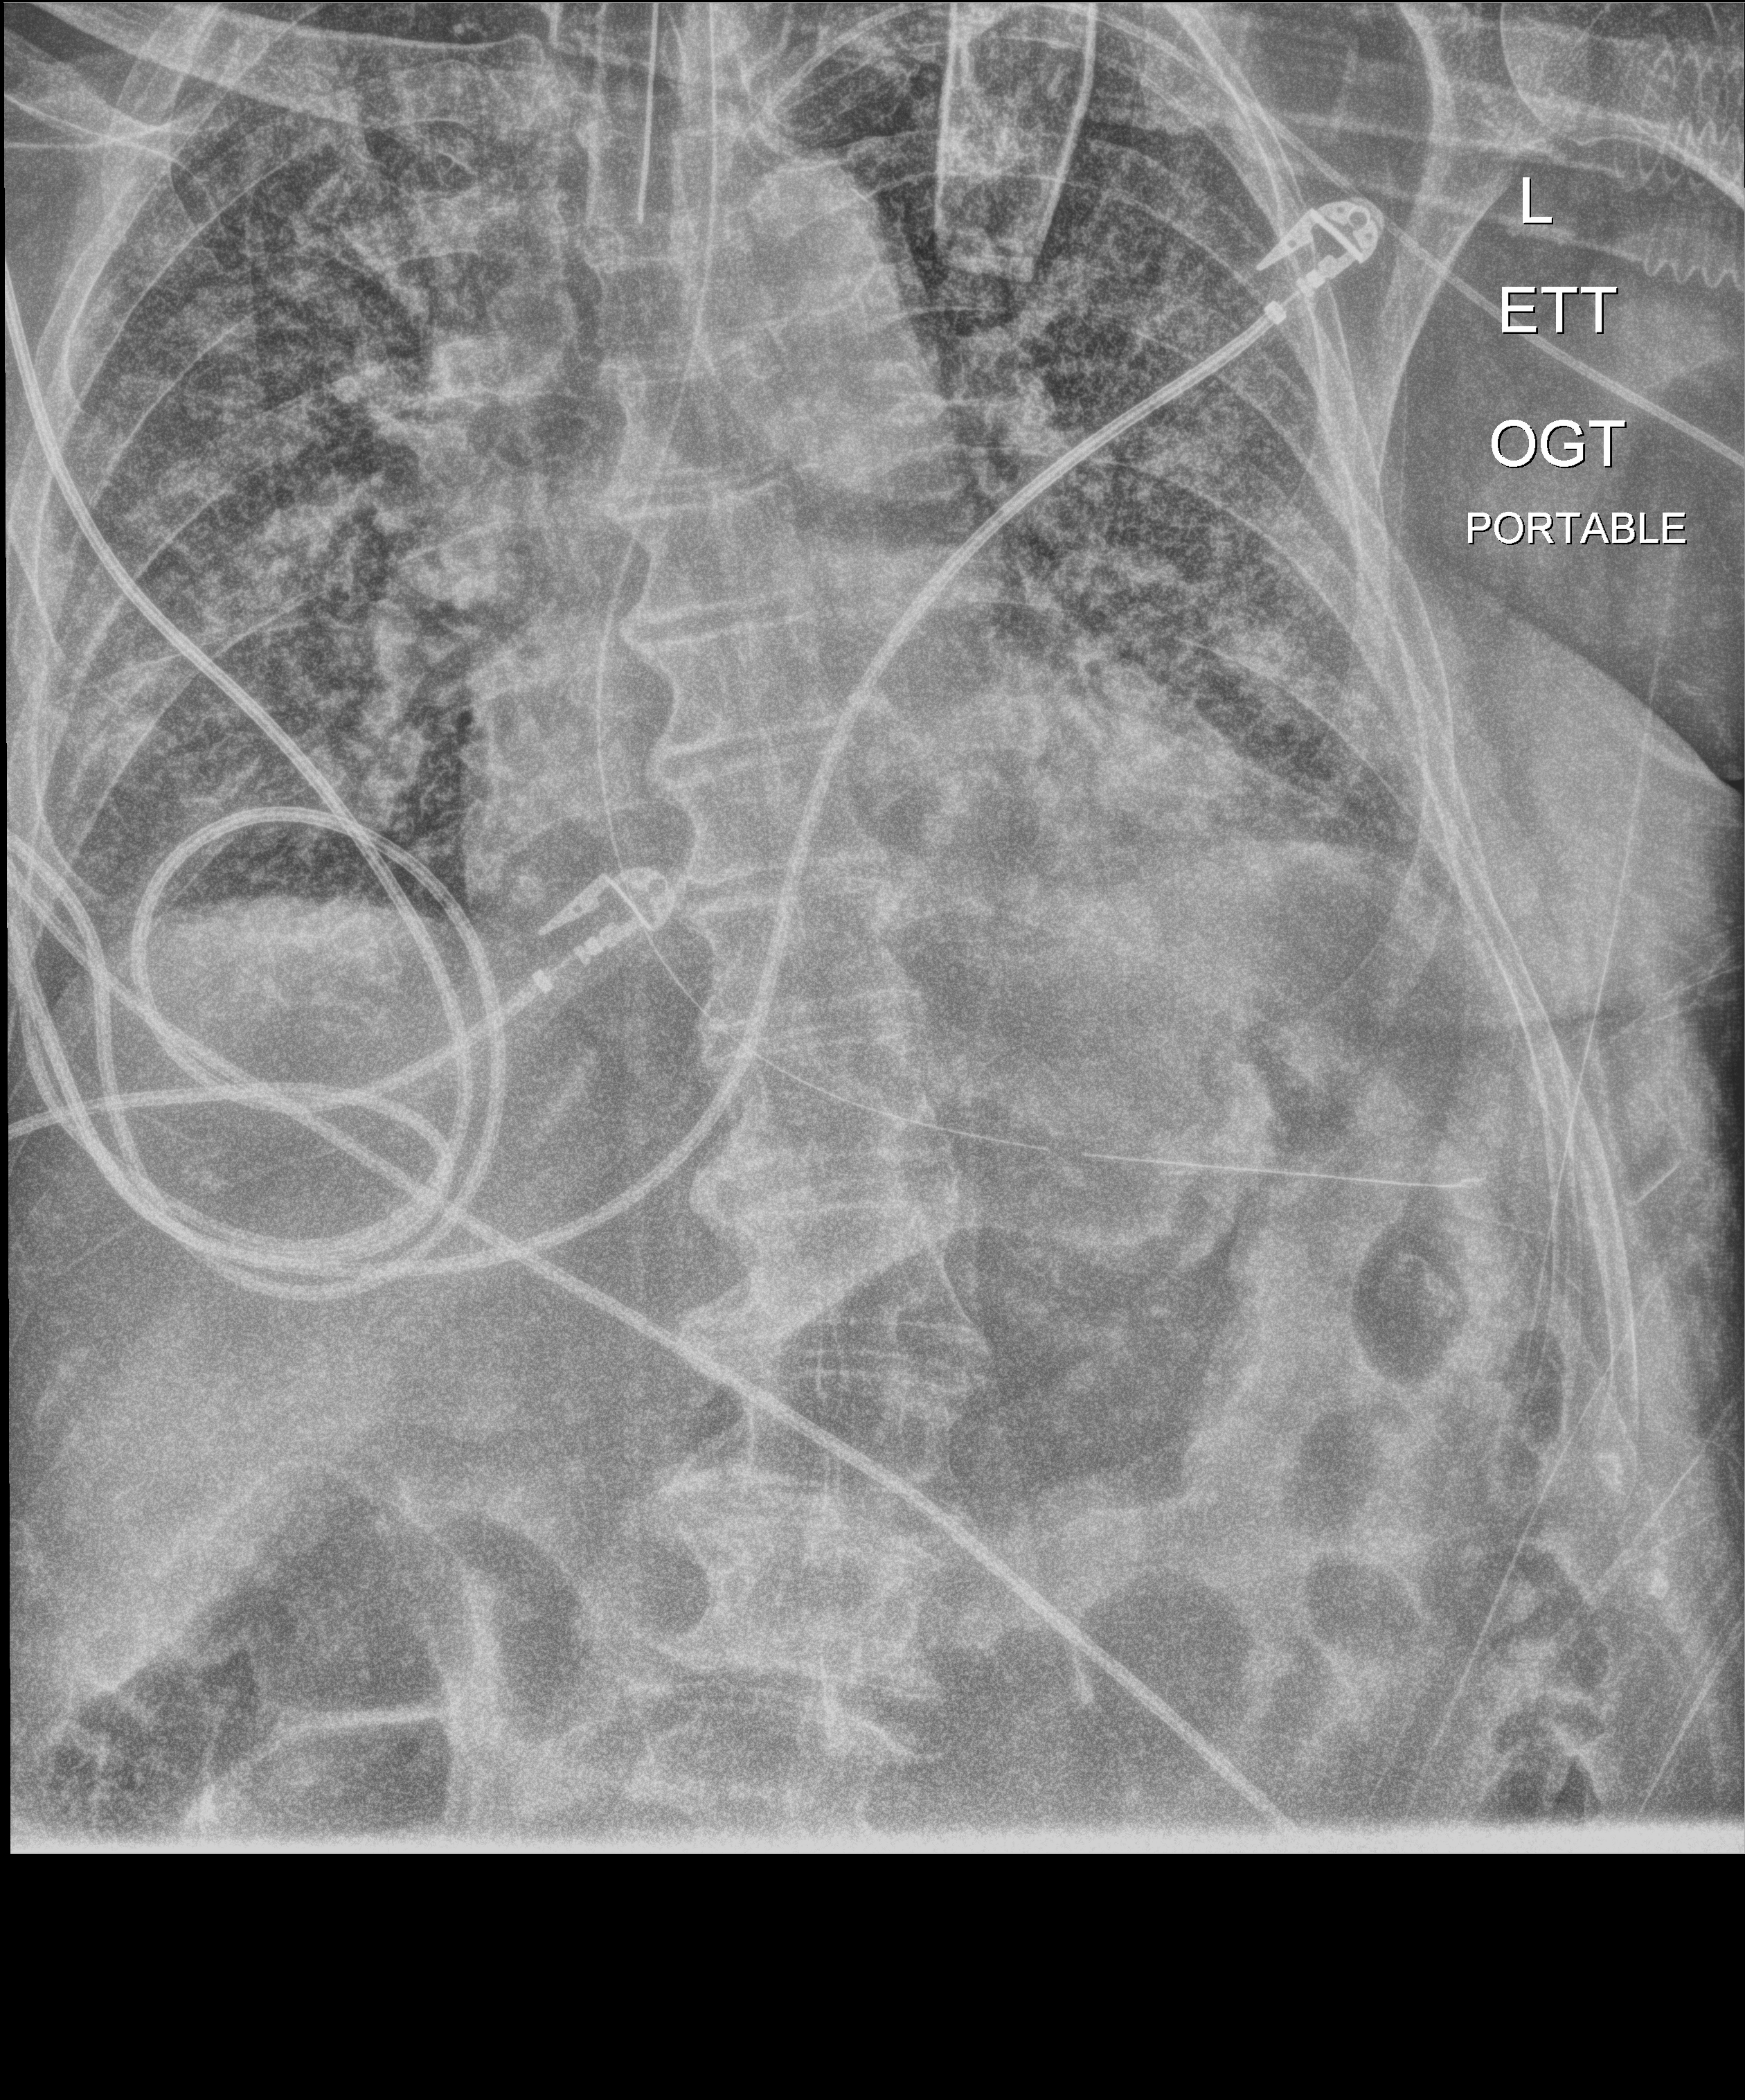
Chest X-ray (portable), anteroposterior (AP) projection. Patient hospitalised with COVID-19; male, aged 75–90 years.
Admission-level facts for this patient (not findings on this image; timing relative to this image not recorded): hypertension (admission record): no; admitted to intensive care during this hospital stay: yes.